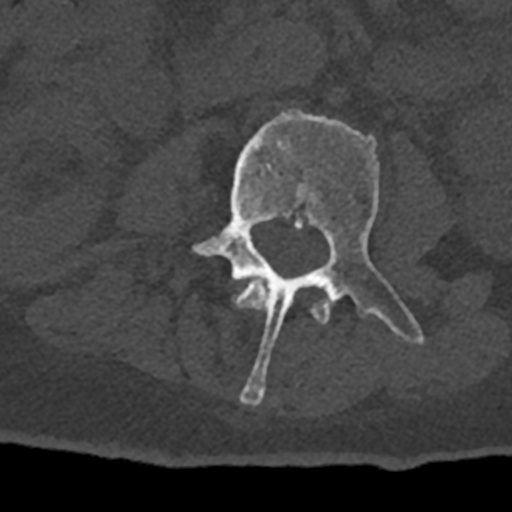
CT including the spine, one axial slice. Slice 321 of 797 in the series (ordered by position). Reconstruction kernel Br40s/3. Bone window (W 1800 / L 400 HU). 0.5 mm slice thickness. 512 × 512 image matrix. Male patient, age 74 years. Case-level facts recorded for this patient, not image findings: primary cancer: renal.
Annotated regions visible in this slice (semi-automatic segmentation, software-assisted and operator-edited):
- L2 vertebra: box from (x=233, y=280) to (x=331, y=324) px
- L3 vertebra: (x=192, y=109)–(x=424, y=405)